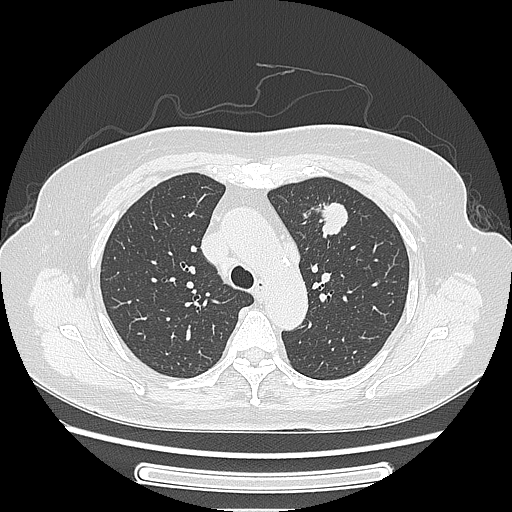
Chest CT, one axial slice; position 172 of 227 along the scan axis; reconstruction kernel LUNG; lung window (W 1500 / L -600 HU); 1.25 mm slice thickness; 512 × 512 image matrix. Female patient, age 77 years. Case-level facts recorded for this patient, not image findings: clinical TNM (as recorded): T1c N3 M0.
Outlined on this slice (rectangle marked by the reading radiologist):
- lung tumour (recorded histology: adenocarcinoma): box from (x=316, y=199) to (x=363, y=248) px